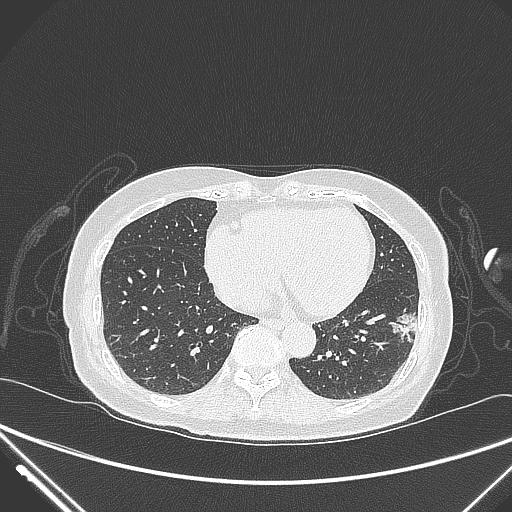
Chest CT, one axial slice; 120 kVp; lung window (W 1500 / L -600 HU); 1 mm slice thickness; 512 × 512 image matrix, field of view 377 × 377 mm. Female patient, age 82 years. From the clinical record (not read from this slice): clinical TNM (as recorded): T1c N0 M0; histopathological grade: G2.
Outlined on this slice (rectangle marked by the reading radiologist):
- lung tumour (recorded histology: adenocarcinoma): bounding box <391,300,422,347> (left, top, right, bottom; pixels)